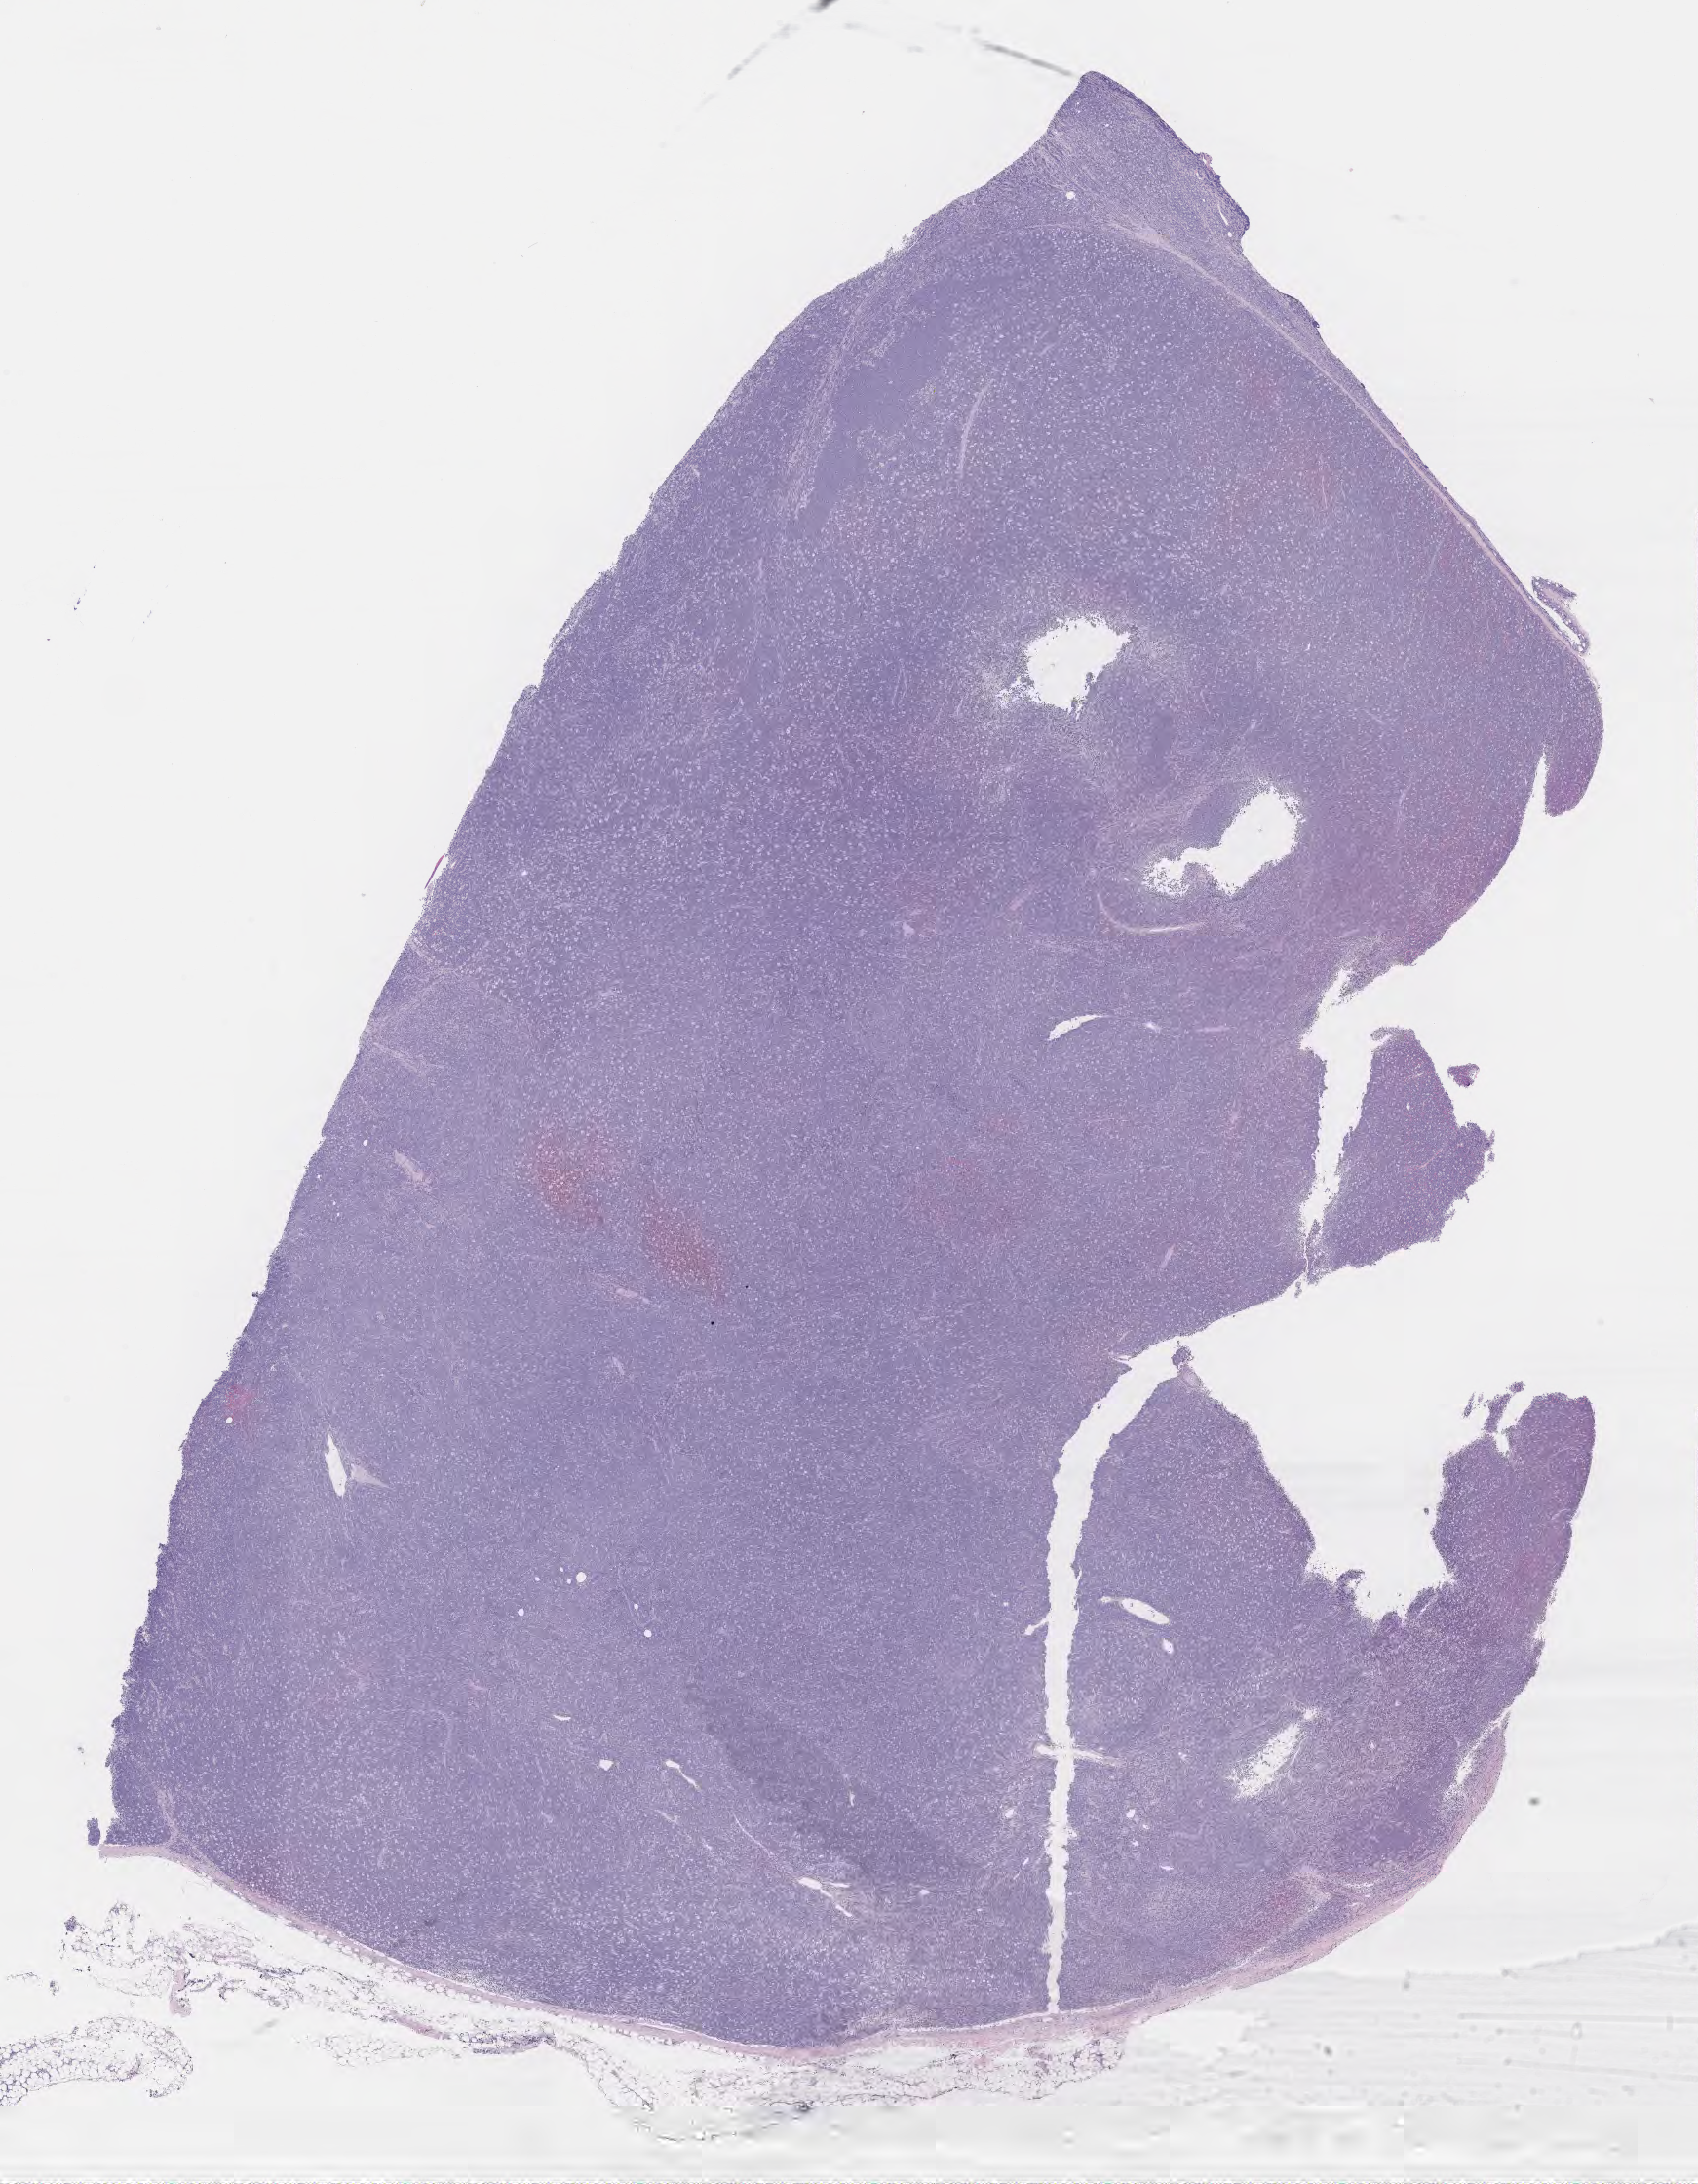
Haematoxylin and eosin whole-slide image — shown as a low-resolution overview of the whole scanned area (about 14.1 x 18.1 mm); tumor tissue; anatomic site: lower limb lymph node. Patient: male, aged 61.
Histologic diagnosis: Burkitt lymphoma, NOS.